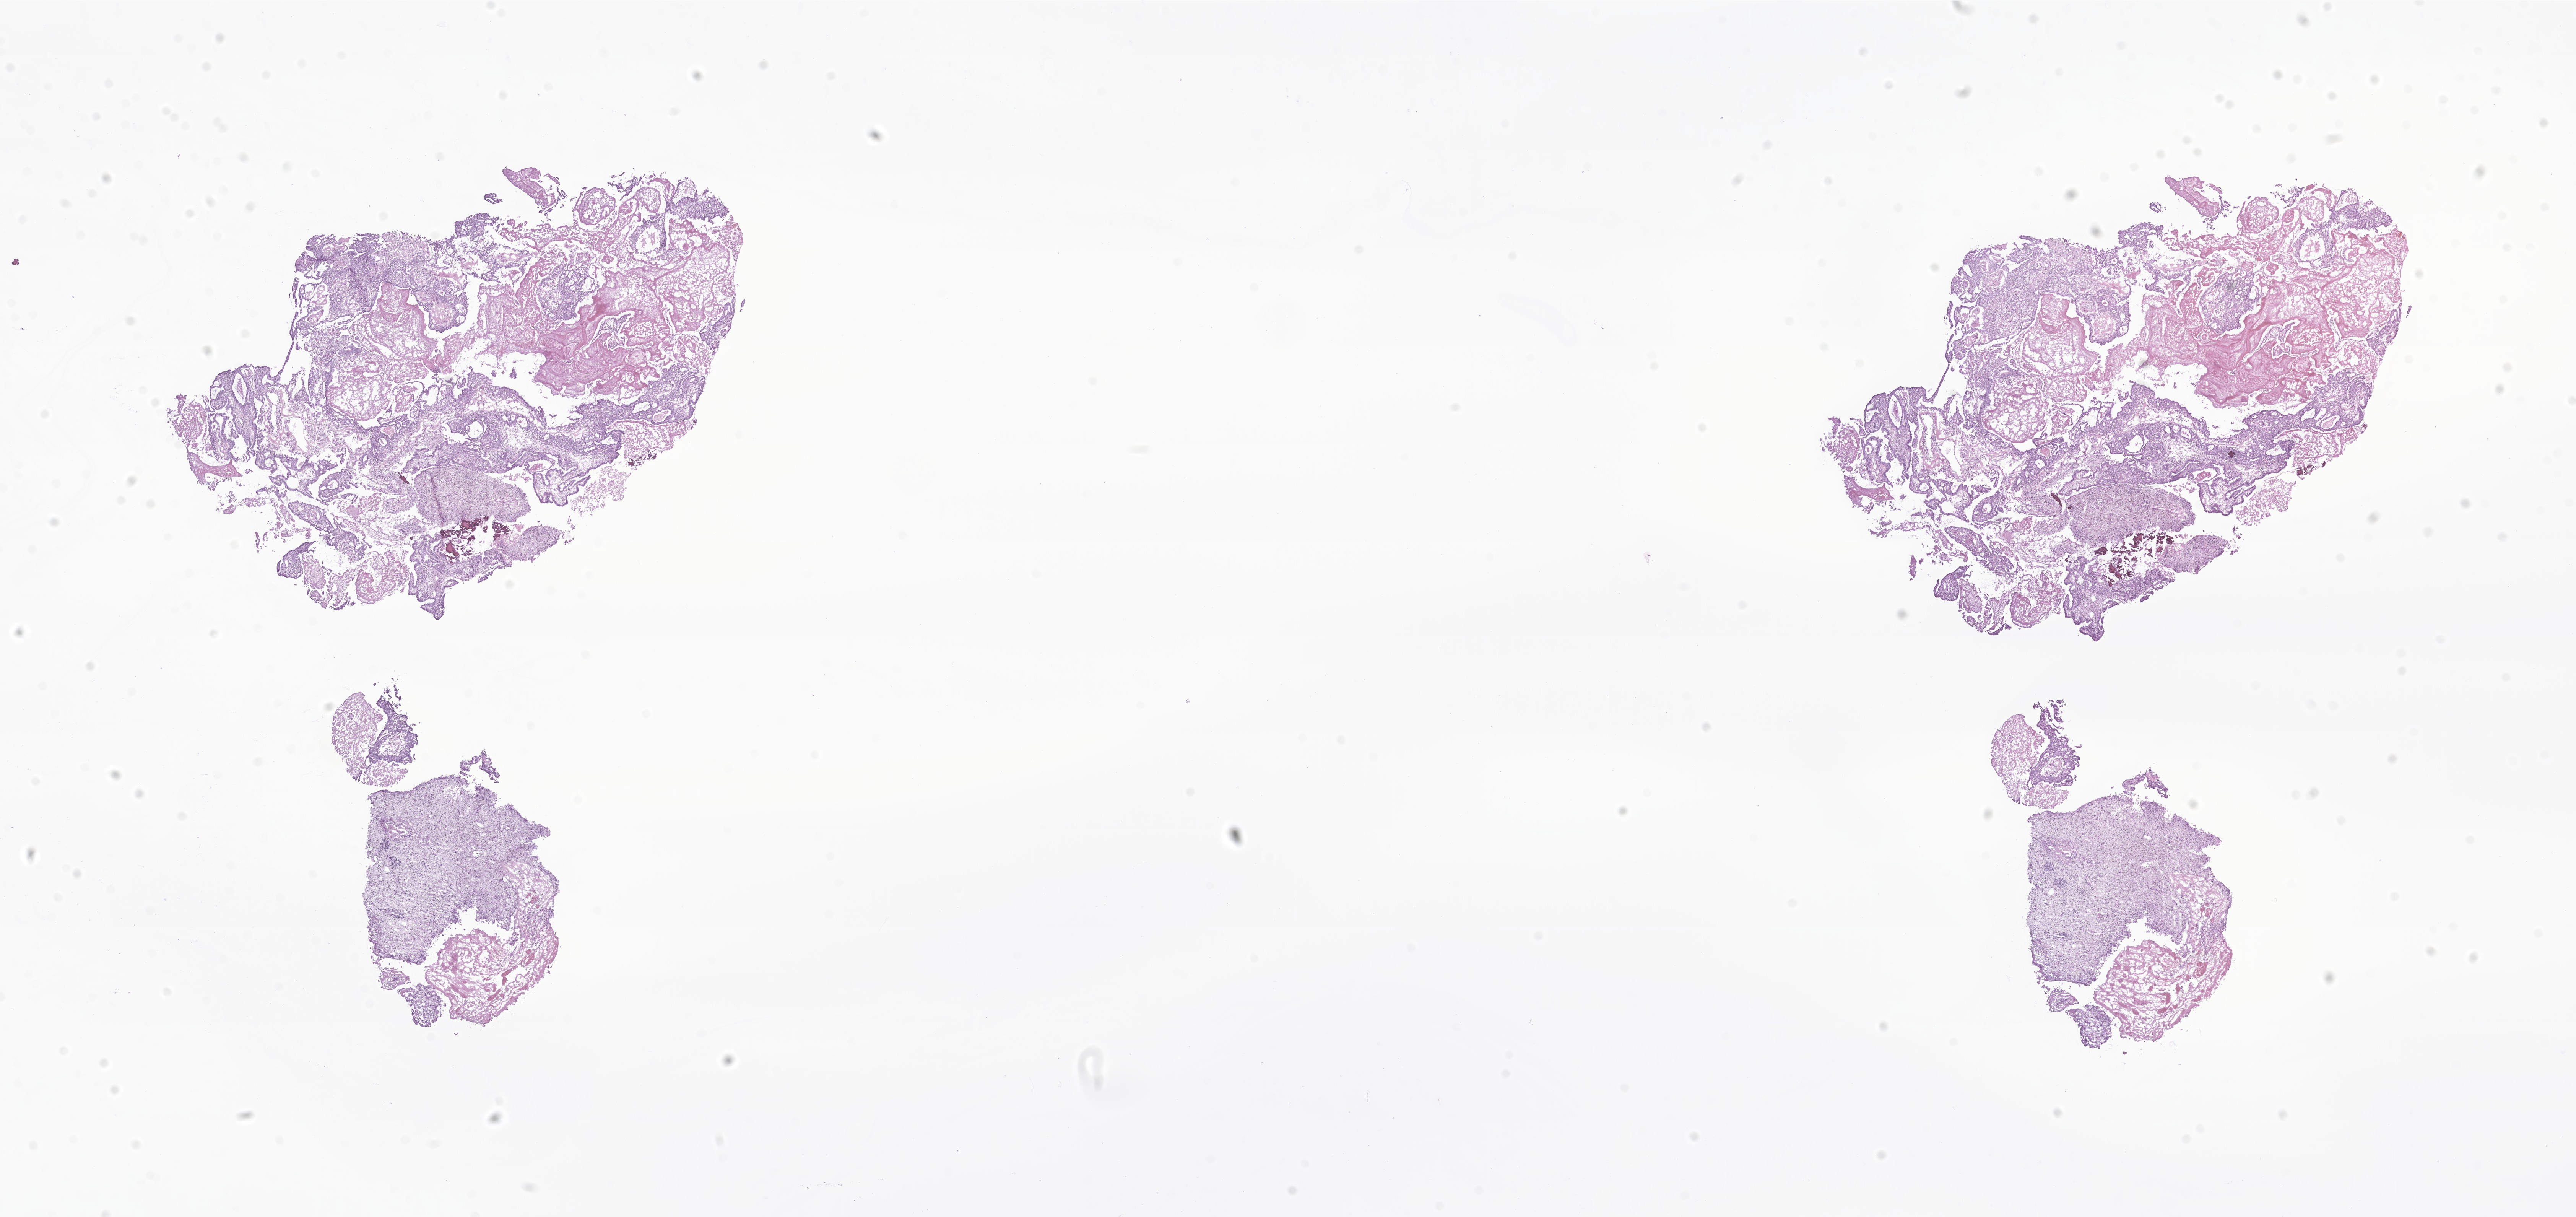
H&E whole-slide image of tumor tissue from the cerebrum, whole scanned area (about 28.4 x 13.4 mm) shown as a low-resolution overview, frozen section. Patient female; age 142 months.
Diagnosis (ICD-O-3 morphology term): Astroblastoma.